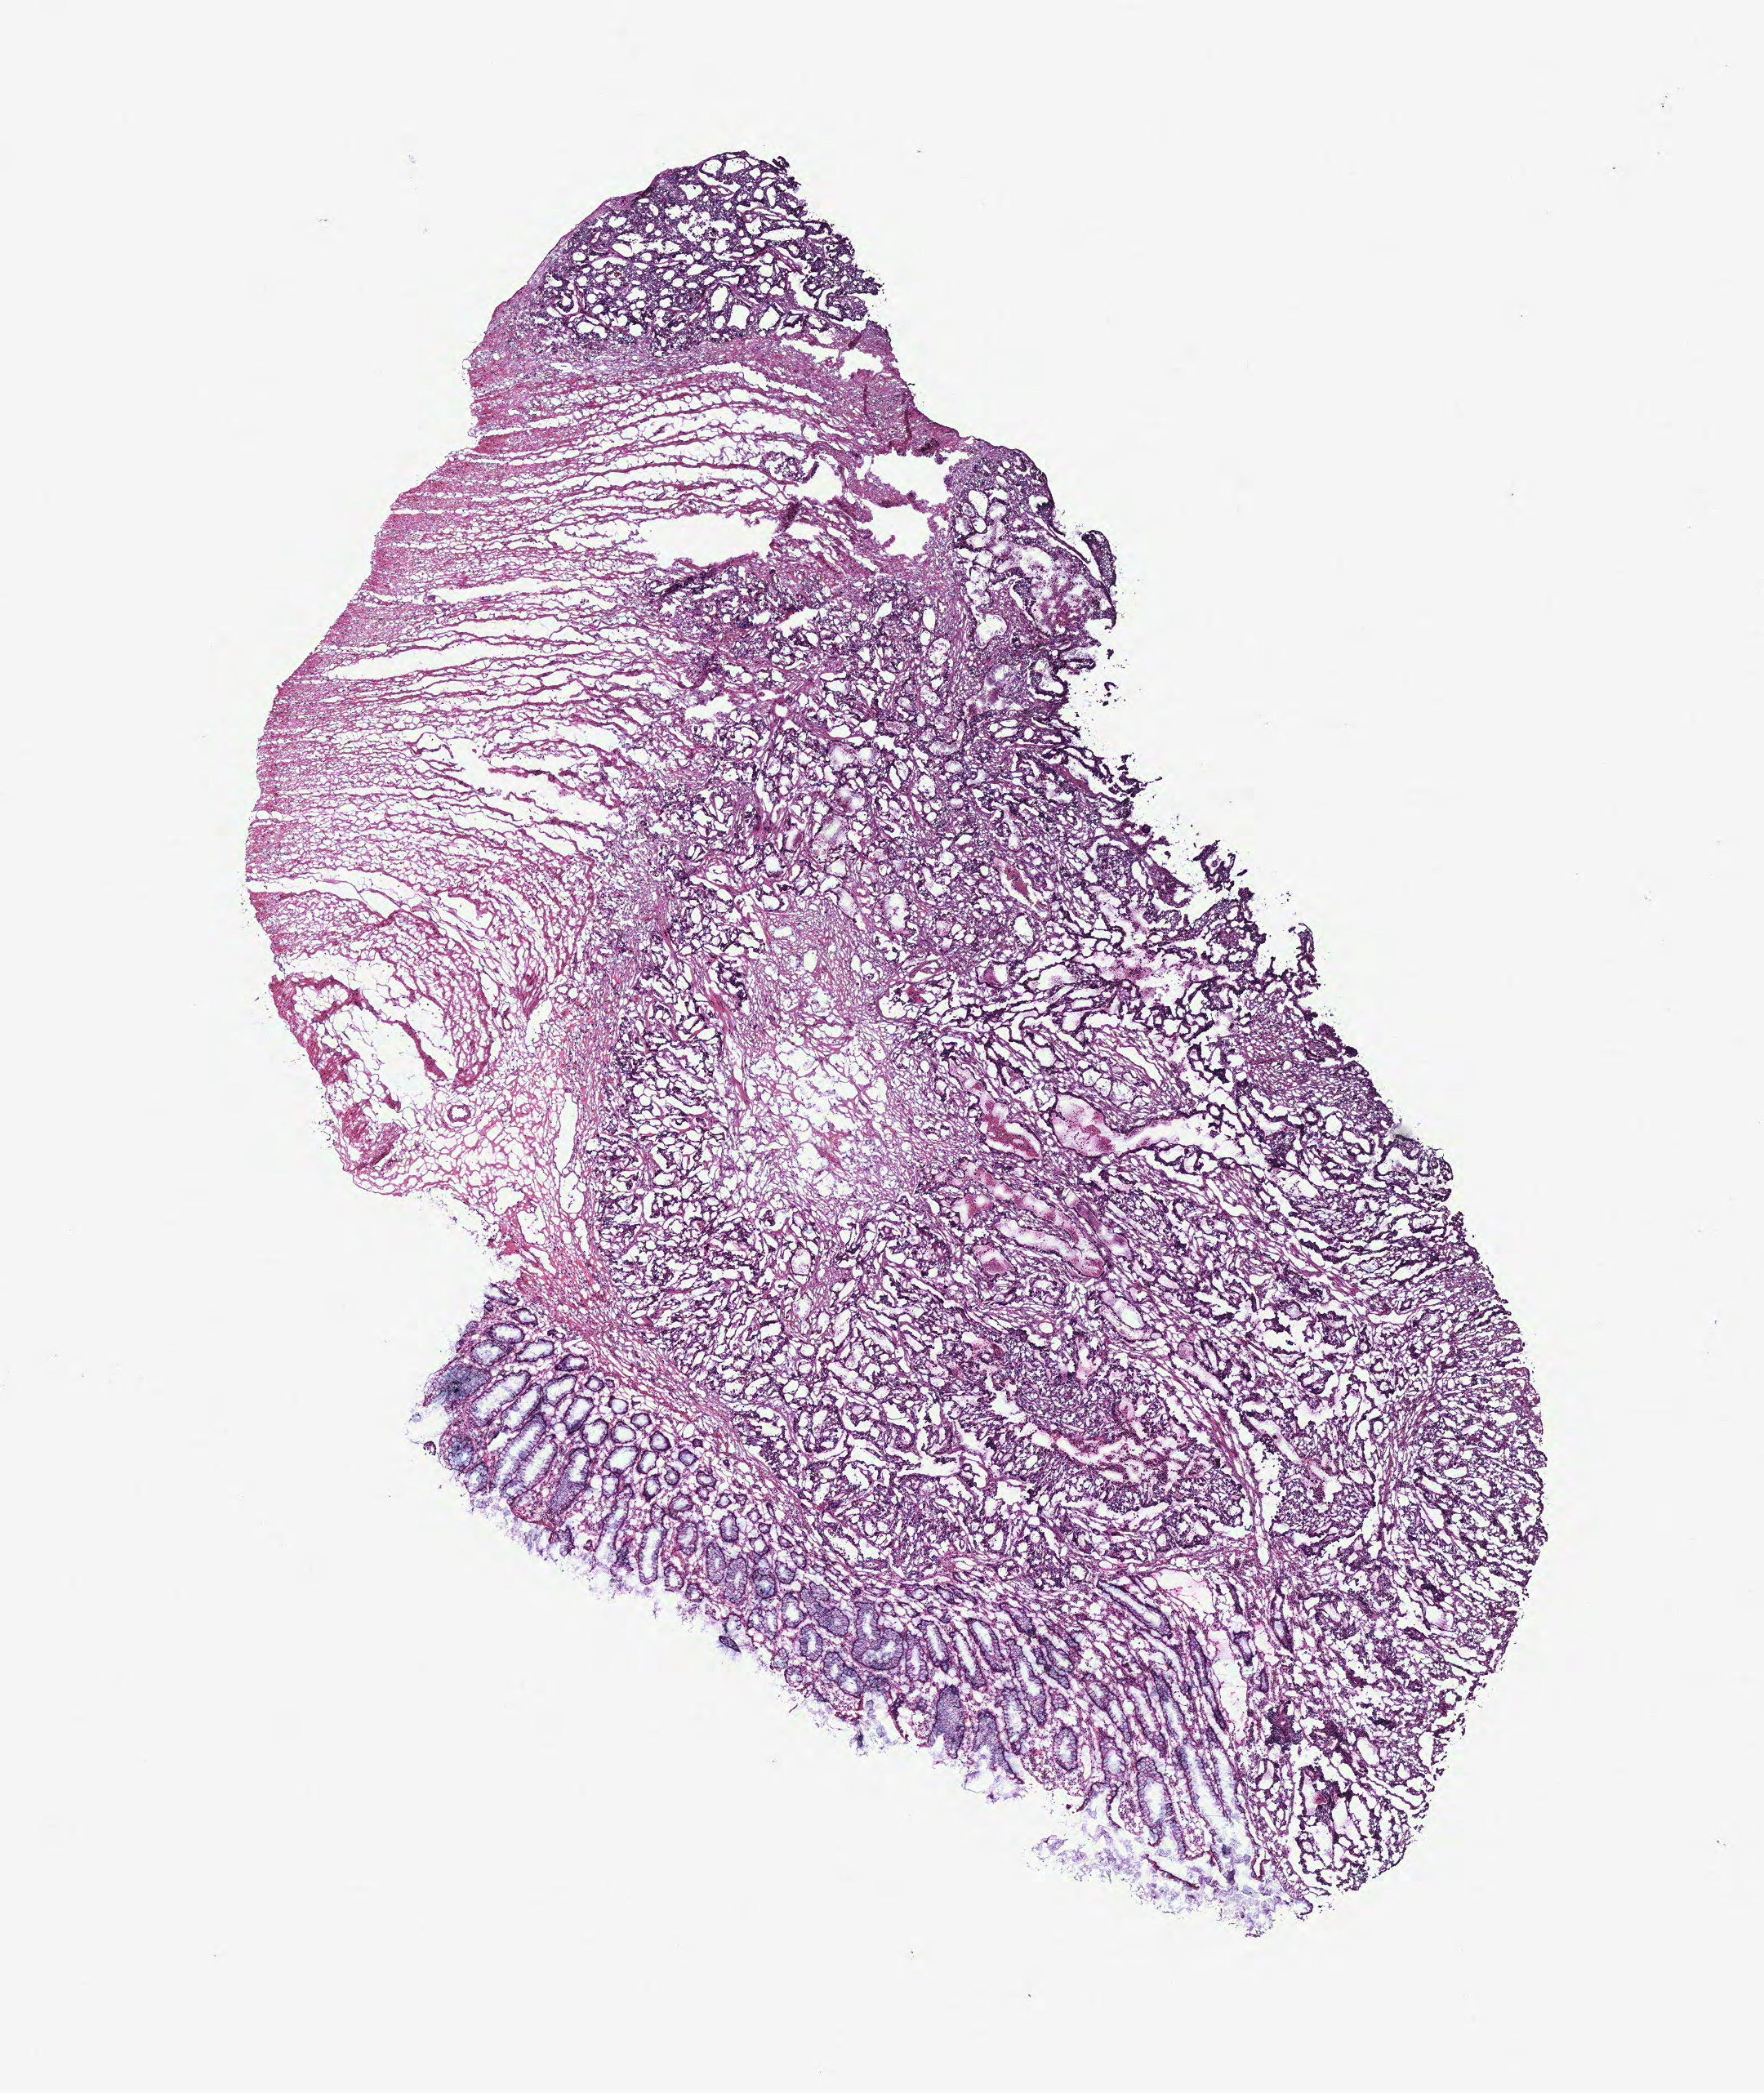
Digitized H&E tissue section (whole slide) — whole scanned area (about 8.6 x 10.3 mm, acquisition: 40x scan) shown as a low-resolution overview, colon, tissue type not recorded.
* patient diagnosis (cohort enrolment): colon cancer (colon)